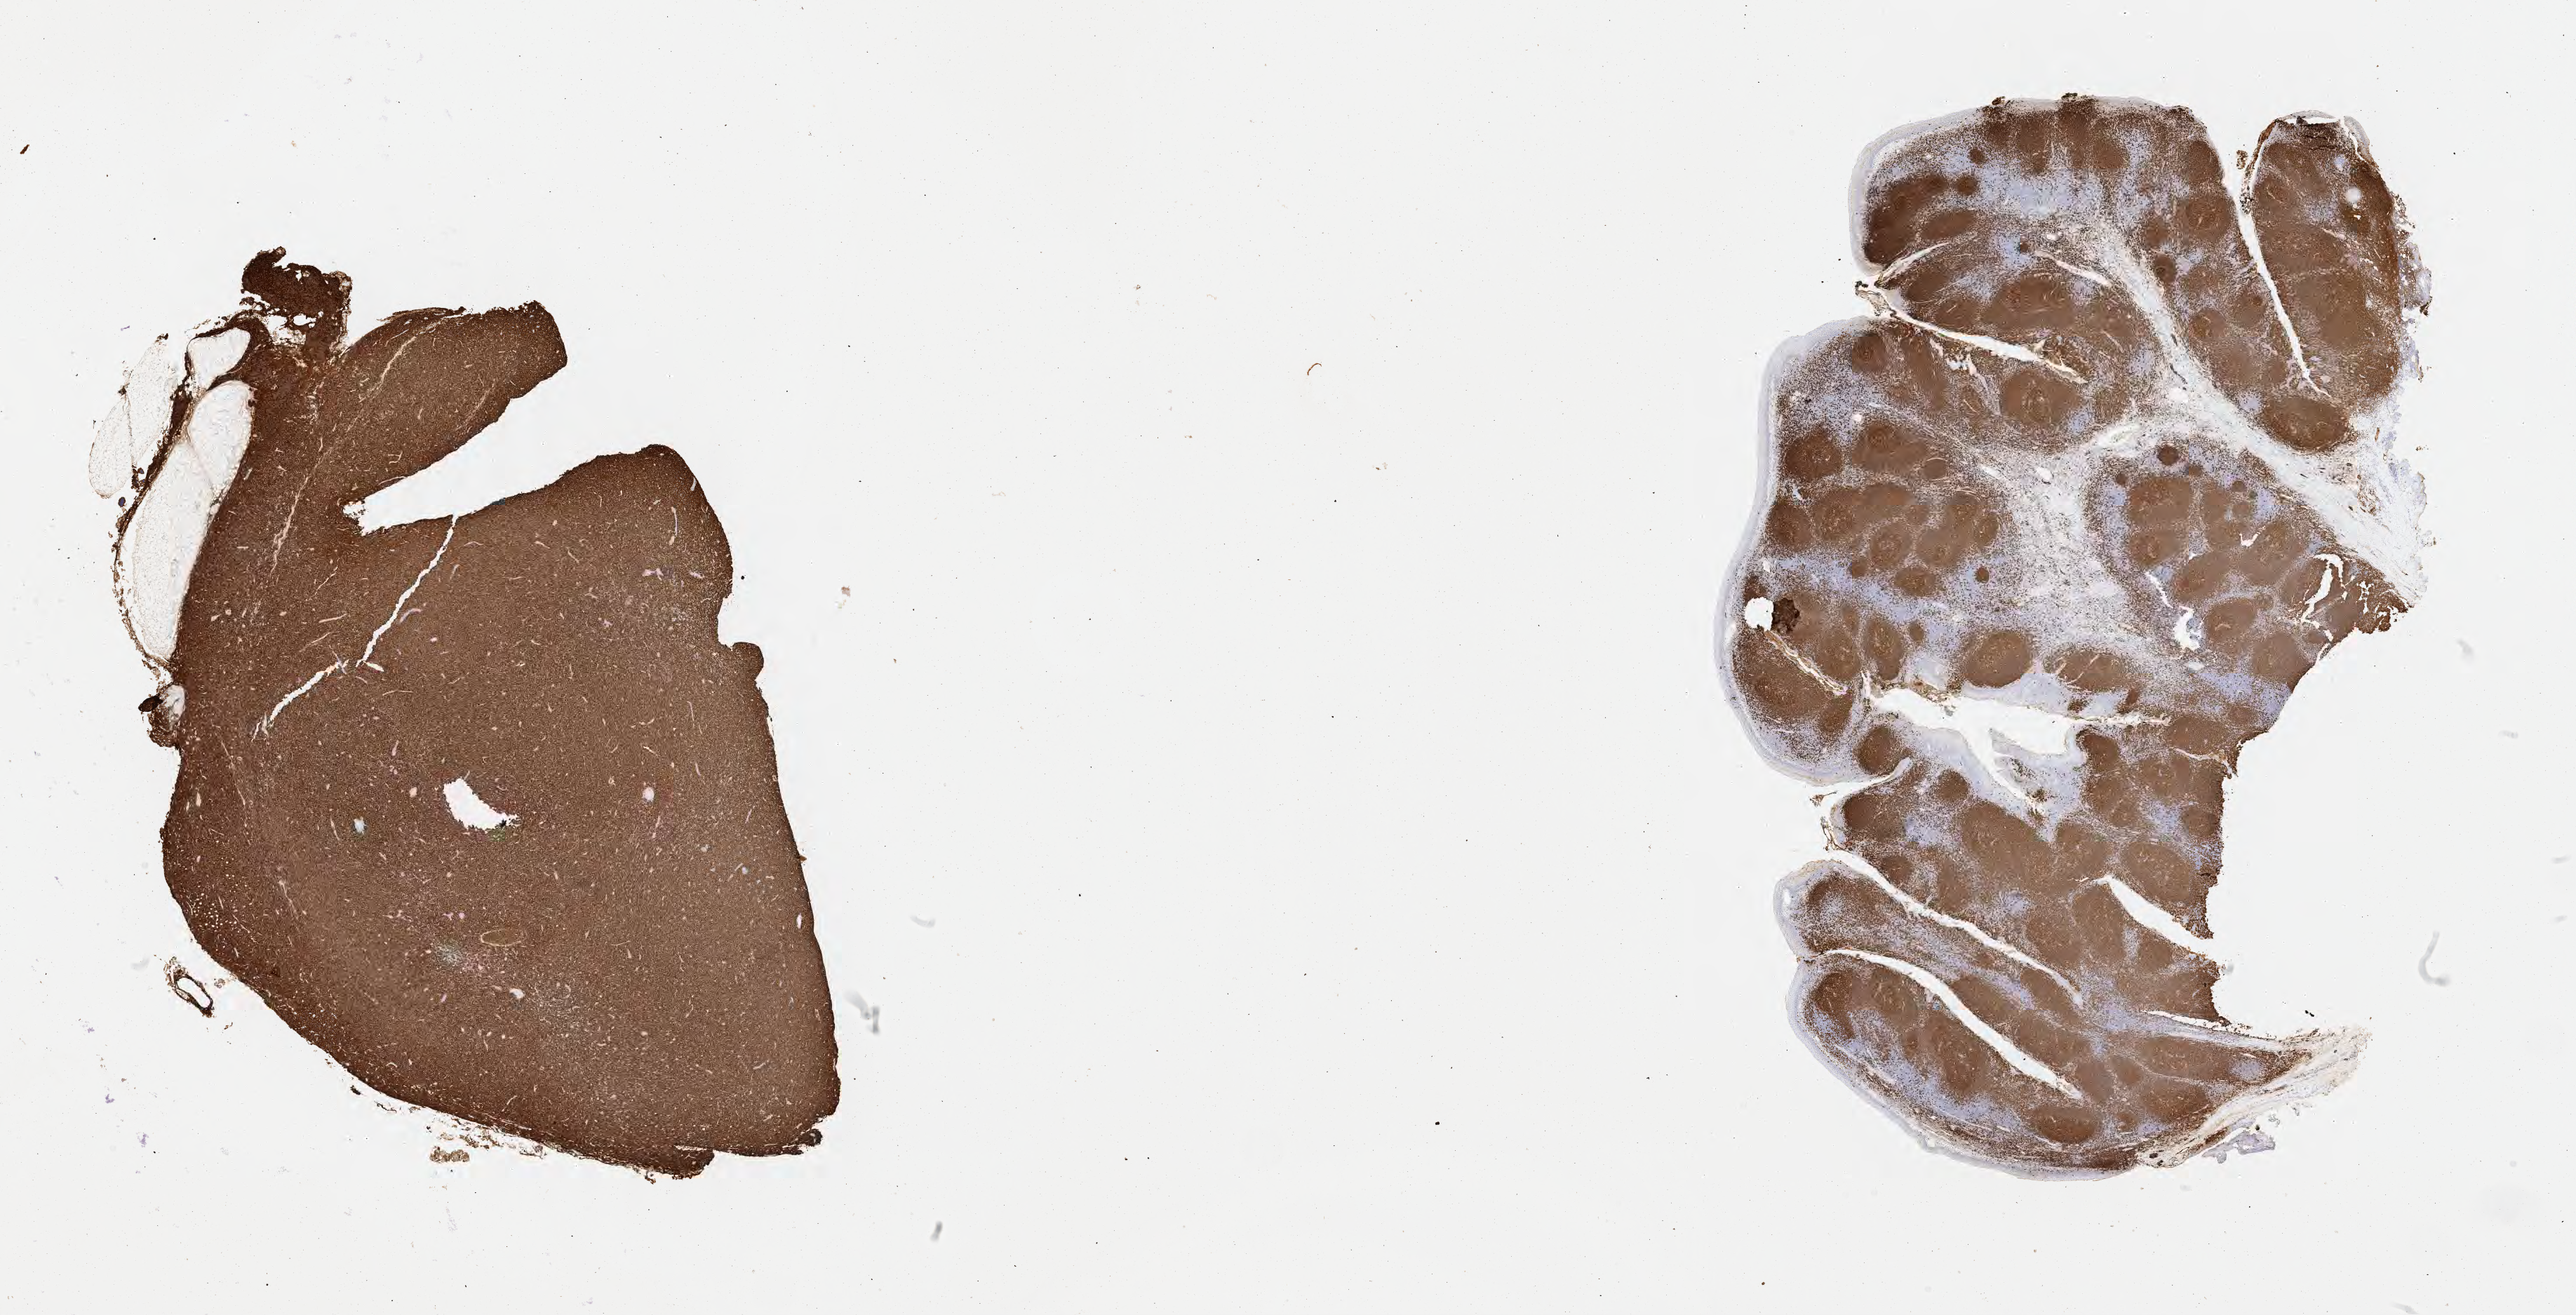
Immunohistochemistry (IHC) whole-slide image stained for CD20 — shown as a low-resolution overview of the whole scanned area (about 29.7 x 15.2 mm), specimen: tumor tissue, site: lymph node. Male patient, age 26 years.
- diagnosis: Diffuse large B-cell lymphoma, NOS